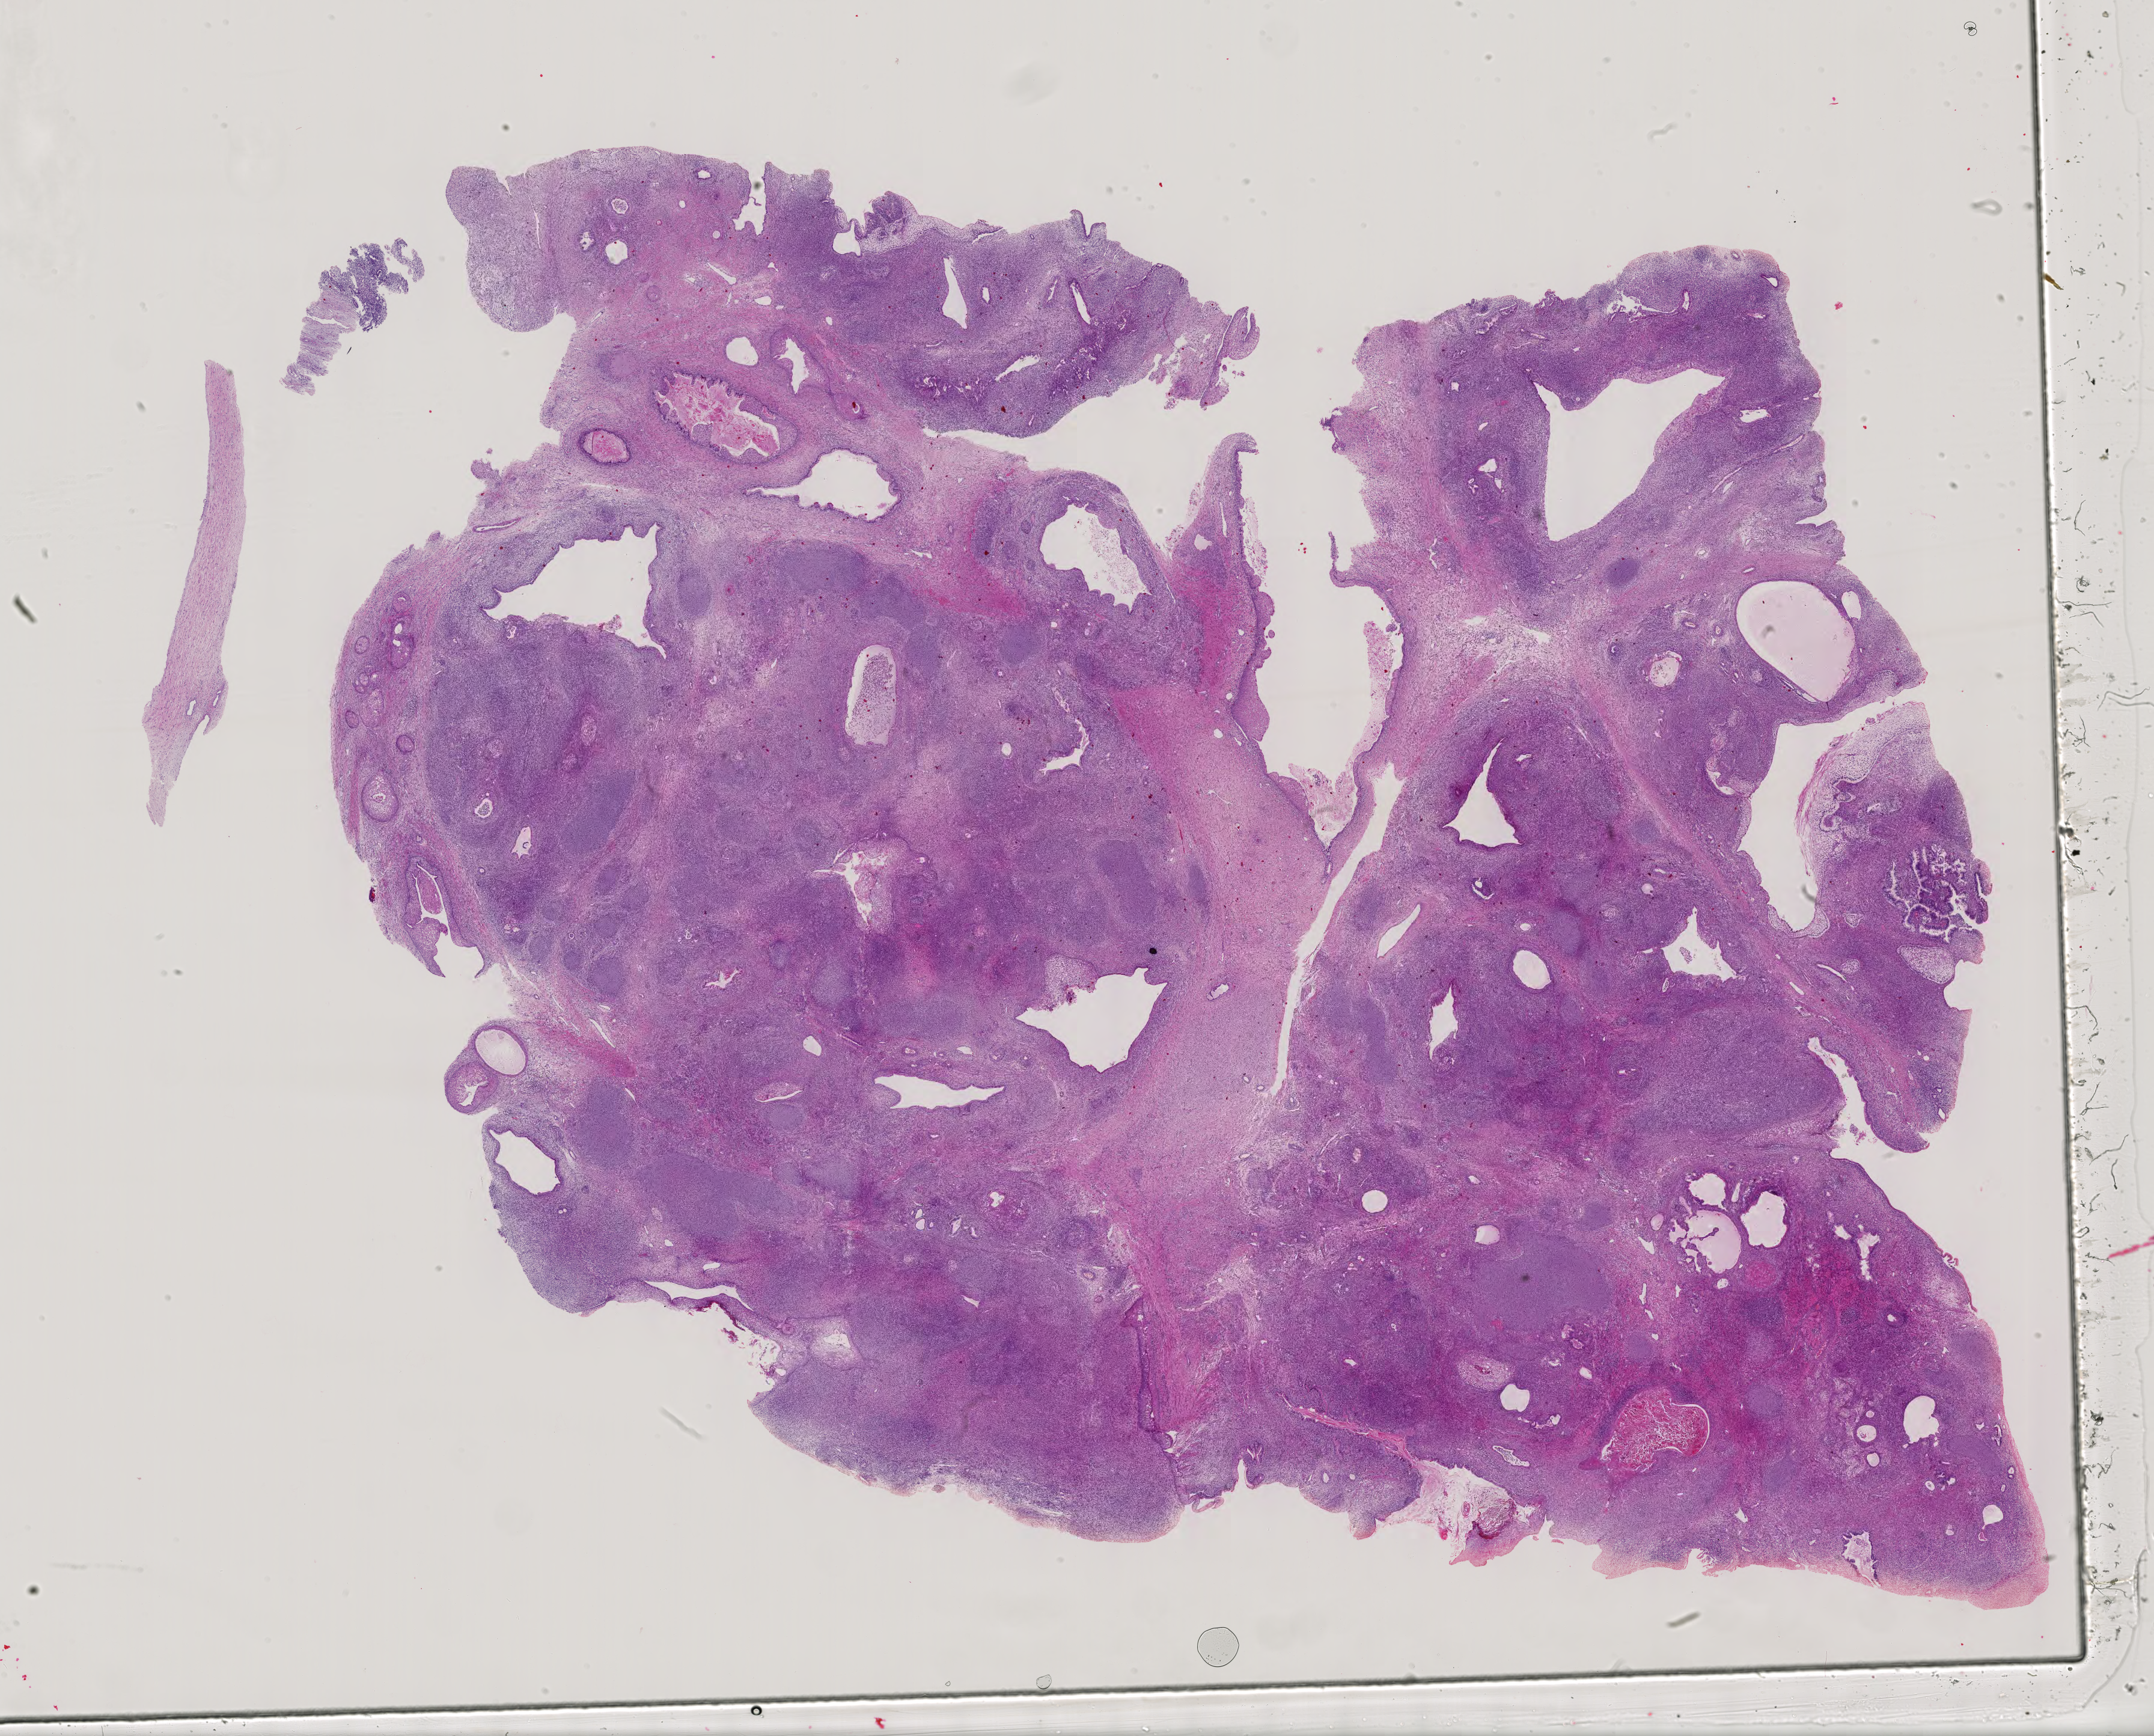
Whole-slide histology image, H&E, shown as a low-resolution overview of the whole scanned area (about 26.1 x 21.0 mm). Male patient.
* specimen: FFPE section; testis, primary tumour sample